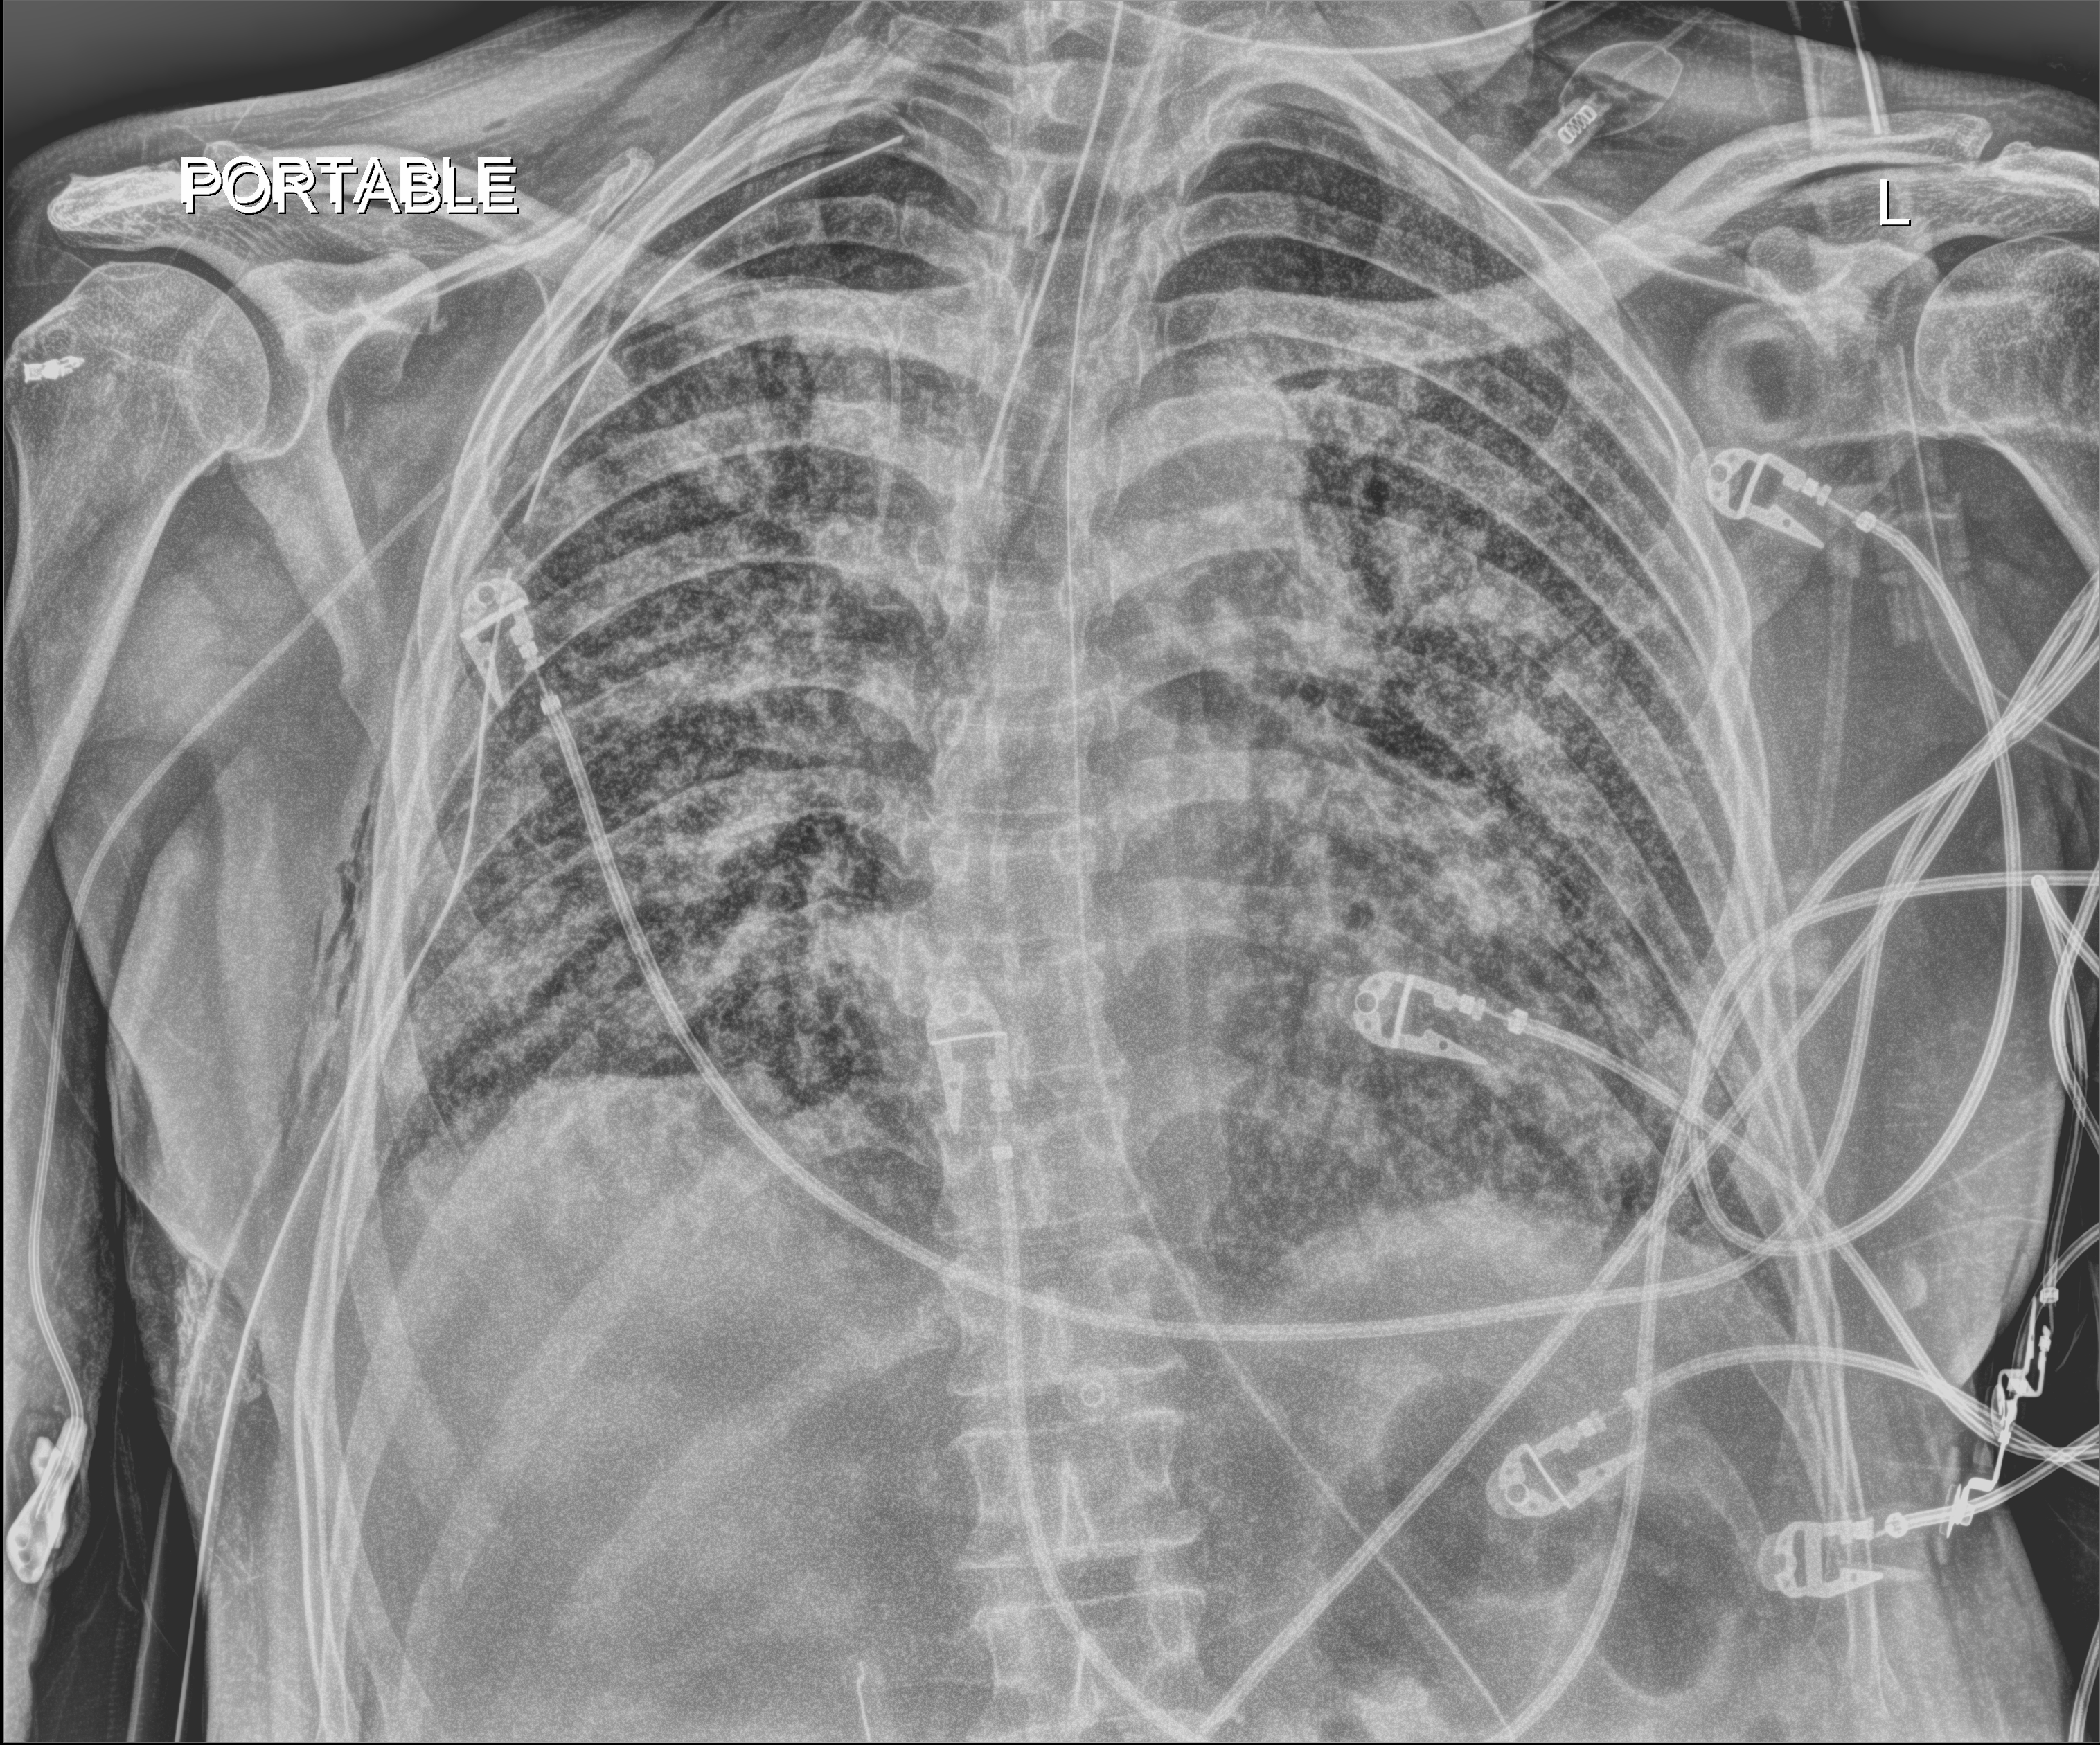
Chest X-ray (portable); anteroposterior (AP) projection. Patient hospitalised with COVID-19; male, aged 60–74 years.
Admission-level facts for this patient (not findings on this image; timing relative to this image not recorded): admitted to intensive care during this hospital stay: yes.